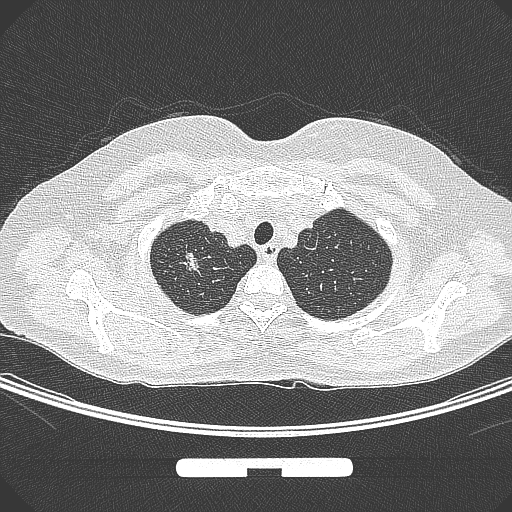
Chest CT, one axial slice; slice 258 of 295 in the series (ordered by position); lung window (W 1500 / L -600 HU); 1 mm slice thickness; 512 × 512 image matrix, field of view 369 × 369 mm. Female patient, age 58 years. Case-level facts recorded for this patient, not image findings: clinical TNM (as recorded): T1b N0 M0.
Outlined on this slice (bounding box drawn by a radiologist):
- lung tumour (recorded histology: adenocarcinoma): bounding box [x1, y1, x2, y2] px = [175, 248, 208, 283]